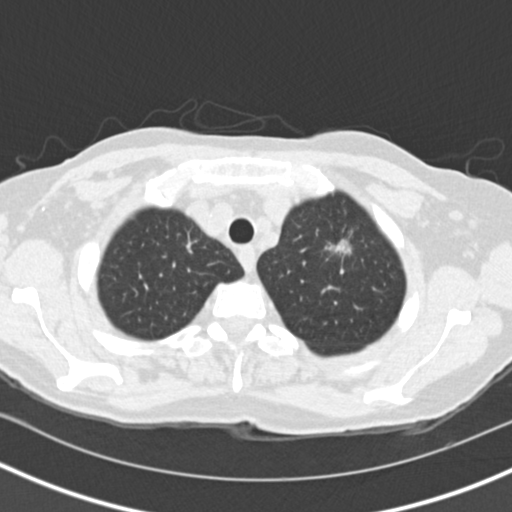
Axial slice from a low-dose chest CT screening exam. First (baseline) screen. Lung window (W 1500 / L -600 HU). 2 mm slice thickness. Standard (soft-tissue) reconstruction kernel (B30f). Slice 23 of 146 in the series. Female, age 73 years at enrolment.
- Expert reader's lesion annotation, bounding box (x1, y1, x2, y2) in pixels: (309, 226, 361, 286).
- Reader record for this screening exam (exam-level; its link to the box is not recorded): non-calcified nodule or mass ≥4 mm, left upper lobe, 27 × 21 mm, spiculated (stellate) margins, soft tissue attenuation.
- Later outcome: lung cancer diagnosed 72 days after this screen — bronchiolo-alveolar adenocarcinoma, NOS, left upper lobe, moderately differentiated (G2), stage IIIB (AJCC 6th edition), 17 mm at pathology.